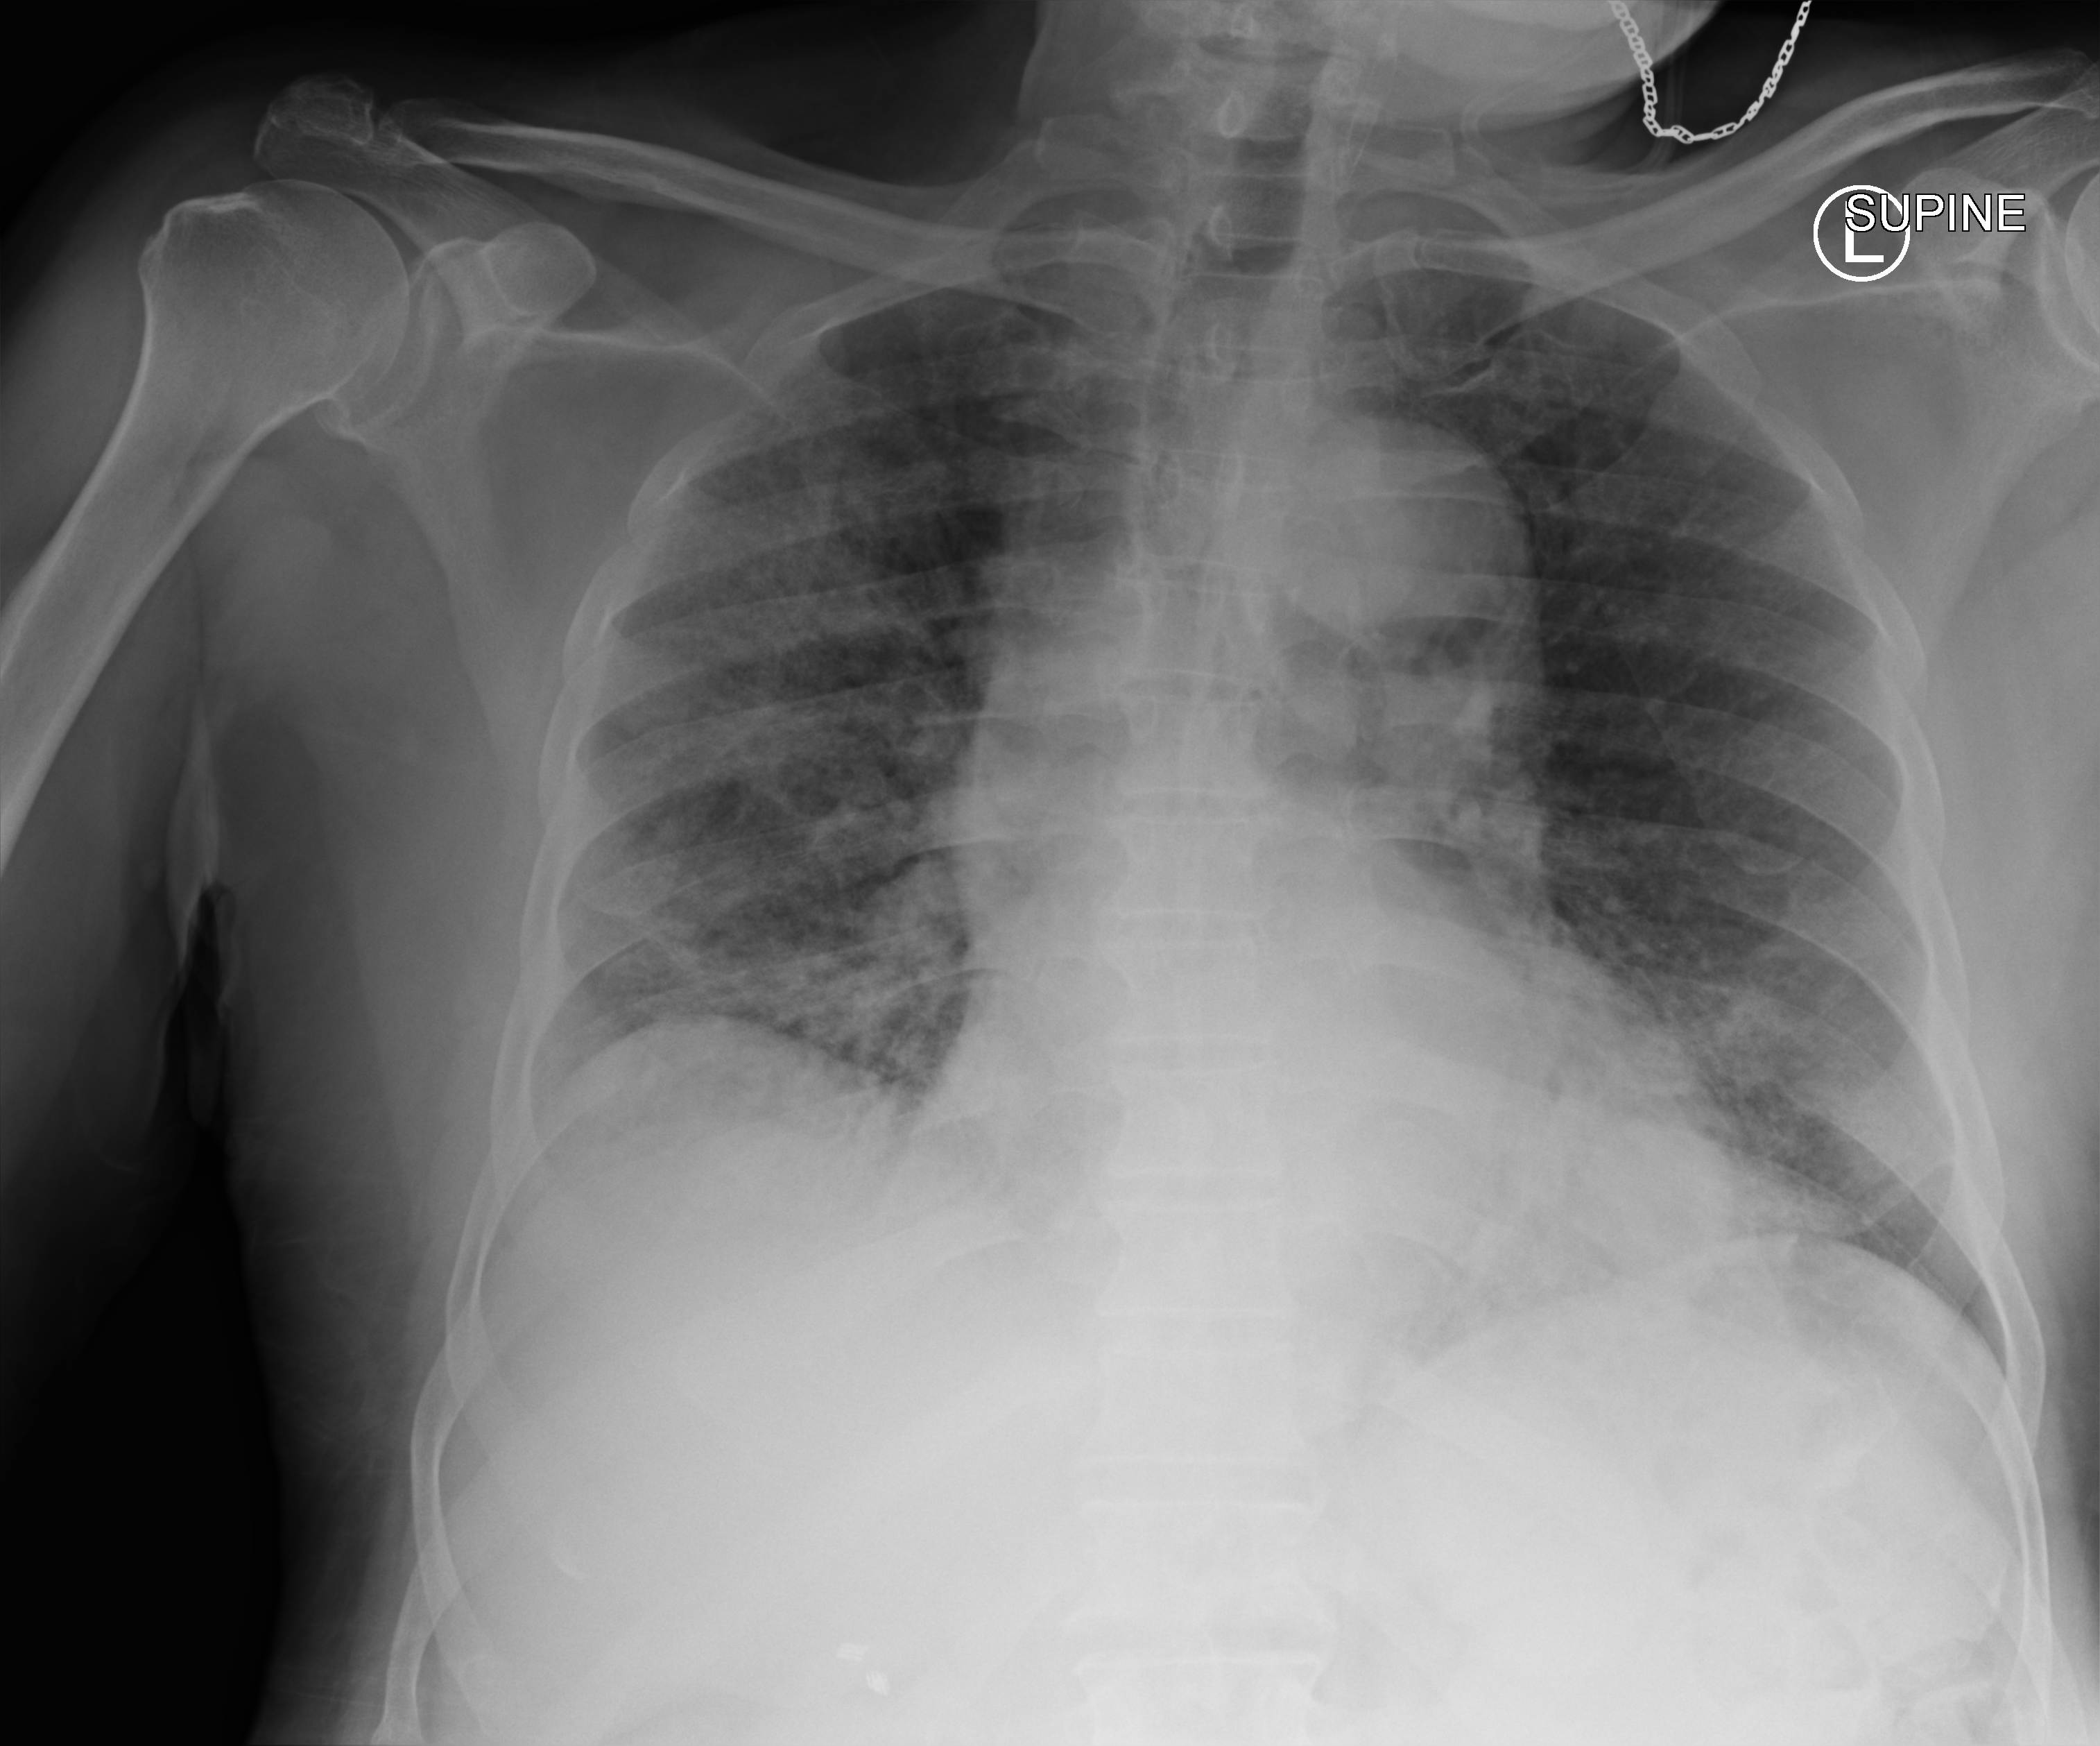
Portable chest radiograph, anteroposterior (AP) projection. Patient hospitalised with COVID-19; male, aged 60–74 years.
Hospital-stay facts (about this admission, not read from this image; timing relative to this image not recorded): mechanically ventilated during this hospital stay: yes.